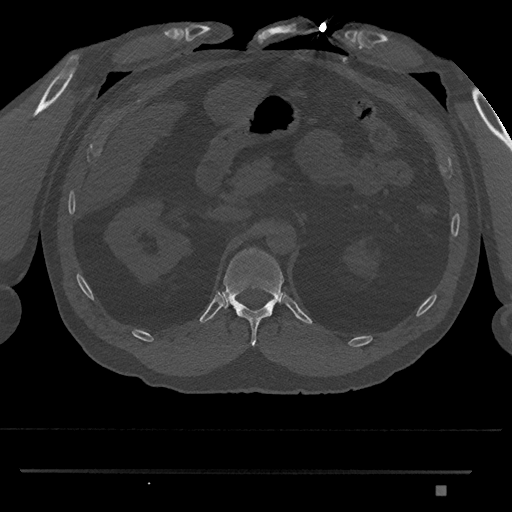
CT including the spine, one axial slice; position 881 of 1134 along the scan axis; reconstruction kernel Br40s/3; 120 kVp; bone window (W 1800 / L 400 HU); 0.5 mm slice thickness; 512 × 512 image matrix, field of view 429 × 429 mm. Patient: male, 65 years. From the clinical record (not read from this slice): primary cancer: prostate.
Structures marked on this image (semi-automatic segmentation, software-assisted and operator-edited):
- T12 vertebra: bounding box (x1, y1, x2, y2) in pixels: (219, 247, 284, 346)